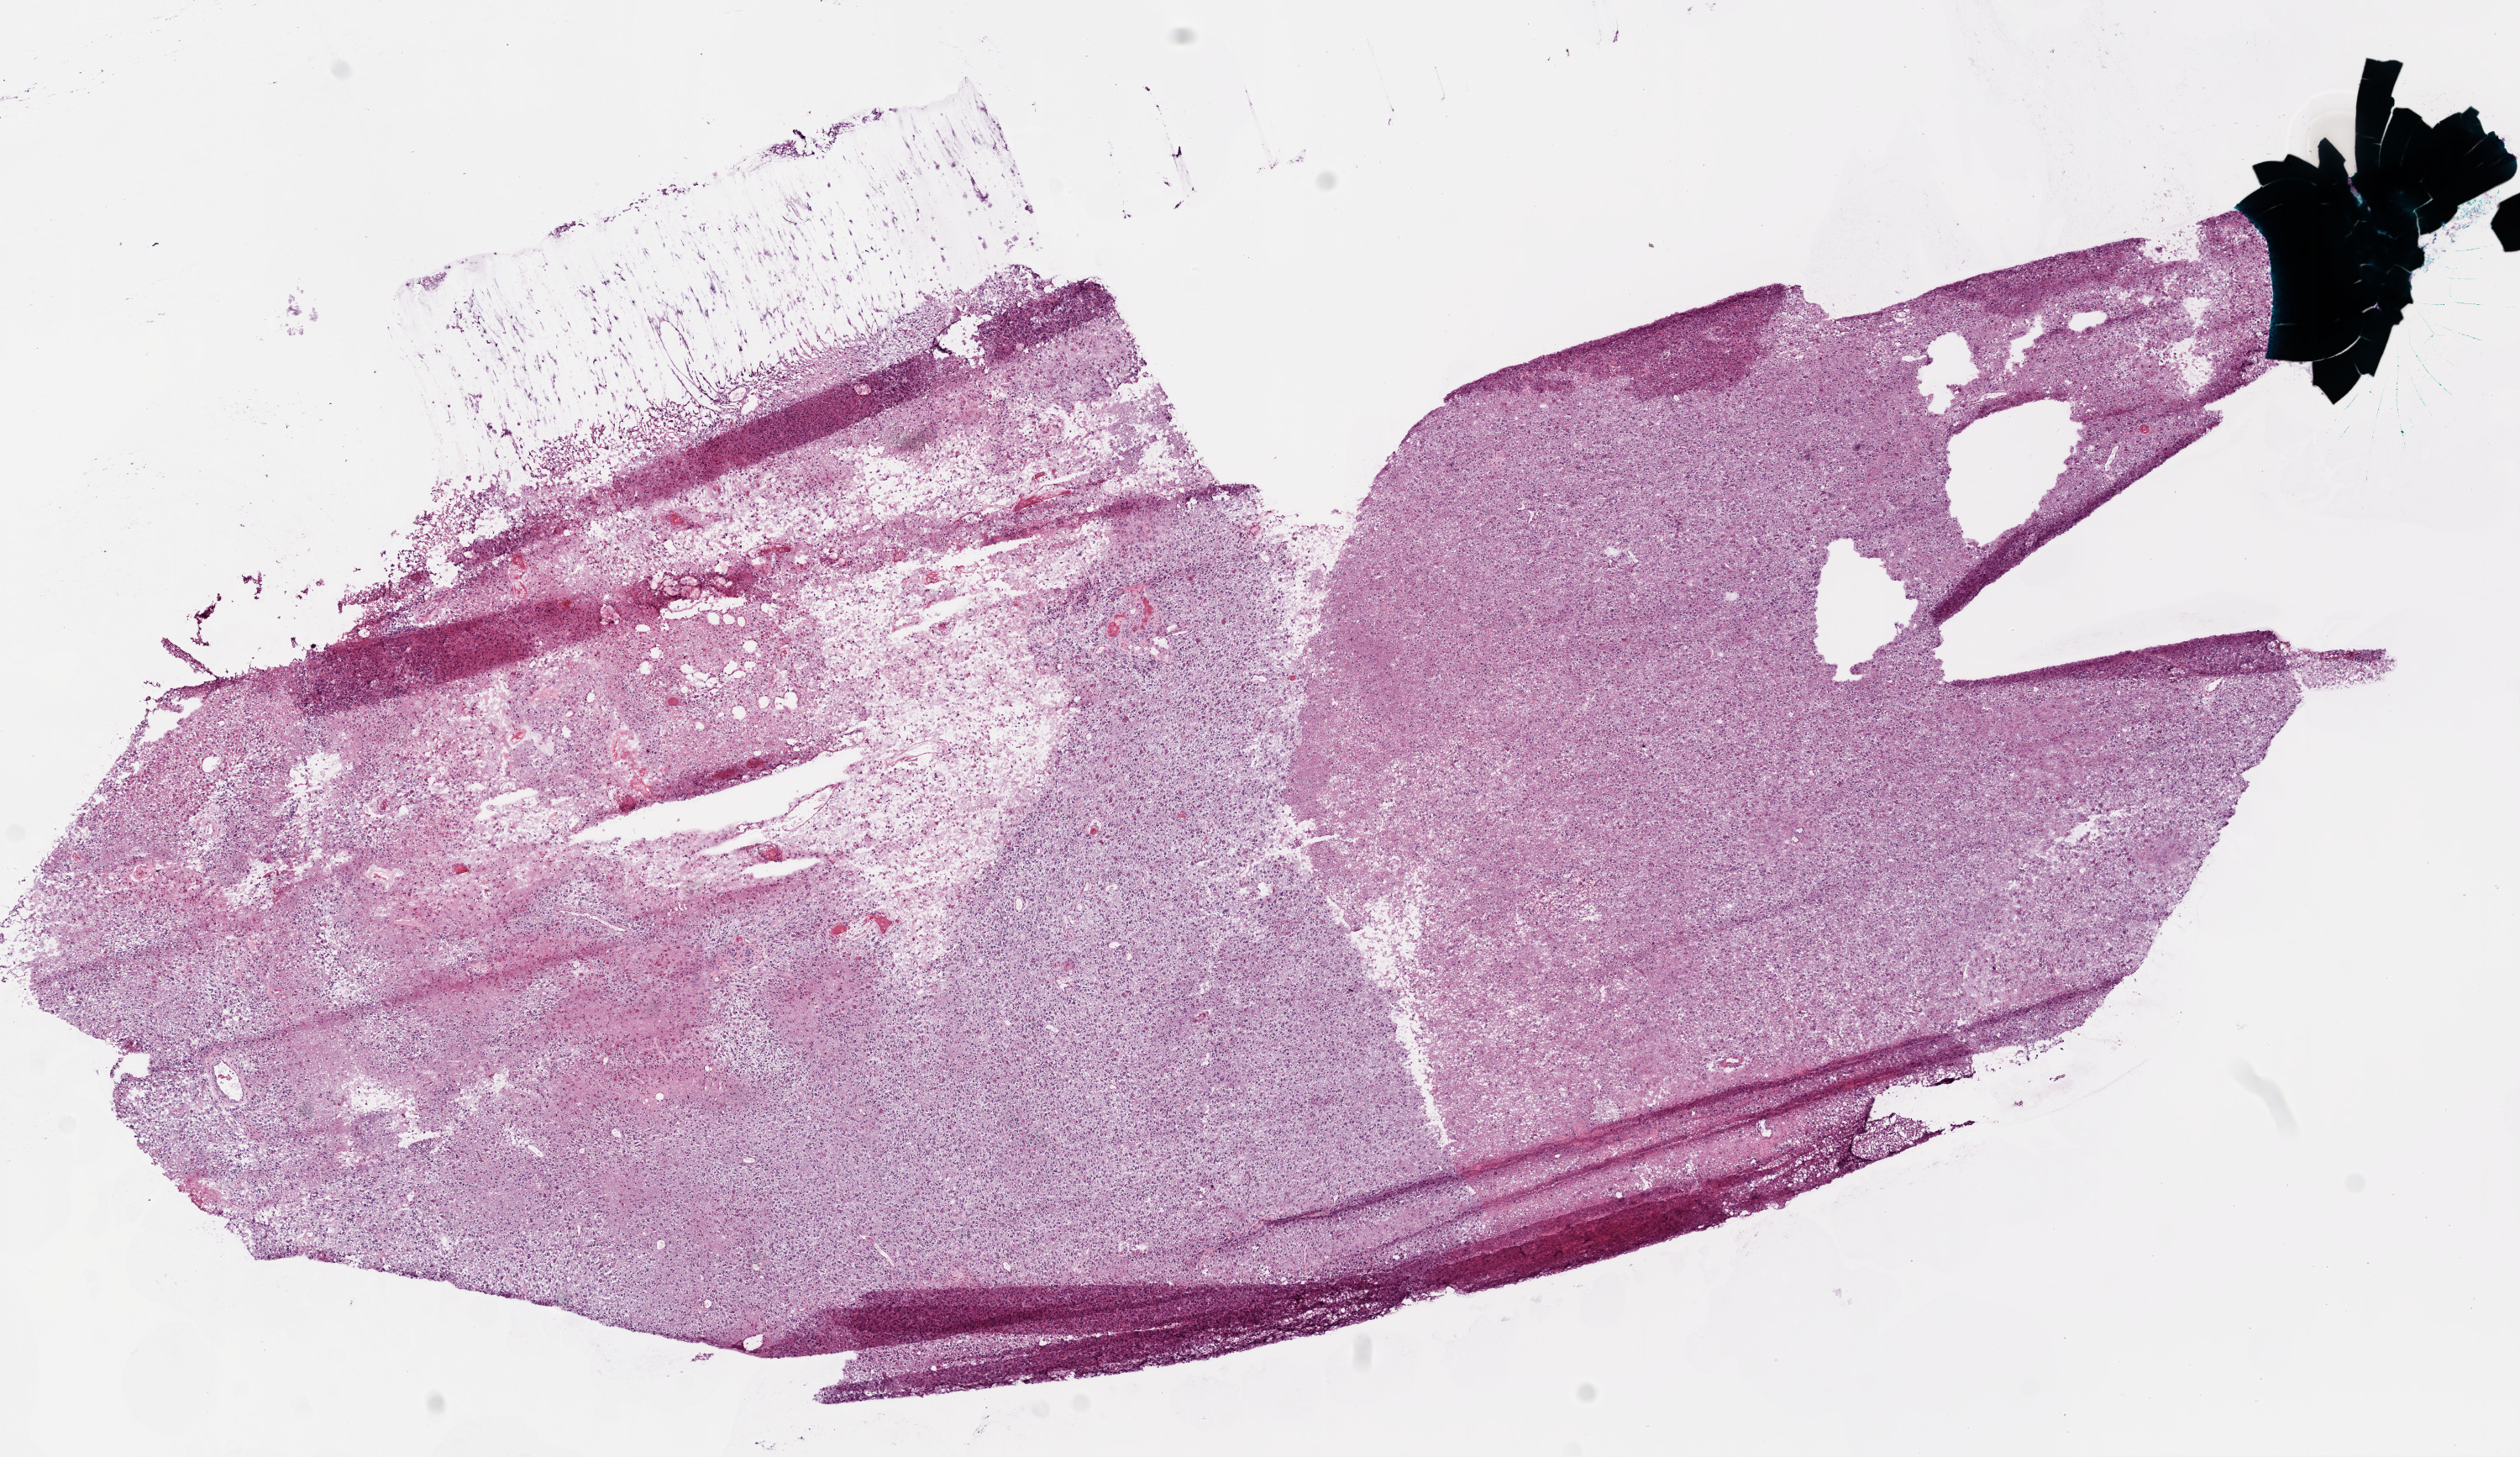
Whole-slide histology image, H&E-stained — a low-resolution overview of the entire scanned area, about 12.0 x 7.0 mm, frozen section from the bottom of the tissue portion, brain, primary tumour sample. Patient: male, age at initial diagnosis 81 years. Pathologist review of this section (percent, as recorded): tumour cells 70%, tumour nuclei 100%, normal cells 0%, stromal cells 0%, necrosis 30%.
Pathologic diagnosis: Glioblastoma.